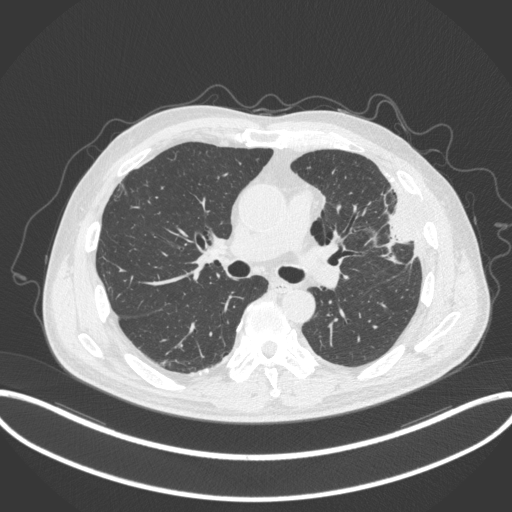
Chest CT, one axial slice. Slice 198 of 382 in the series (ordered by position). Reconstruction kernel B31f. Lung window (W 1500 / L -600 HU). 1 mm slice thickness. 512 × 512 image matrix, field of view 415 × 415 mm. Male patient, age 64 years. Case-level facts recorded for this patient, not image findings: clinical TNM (as recorded): T4 N1 M0.
Structures marked on this image (bounding box drawn by a radiologist):
- lung tumour (recorded histology: adenocarcinoma): bounding box <372,186,411,253> (left, top, right, bottom; pixels)